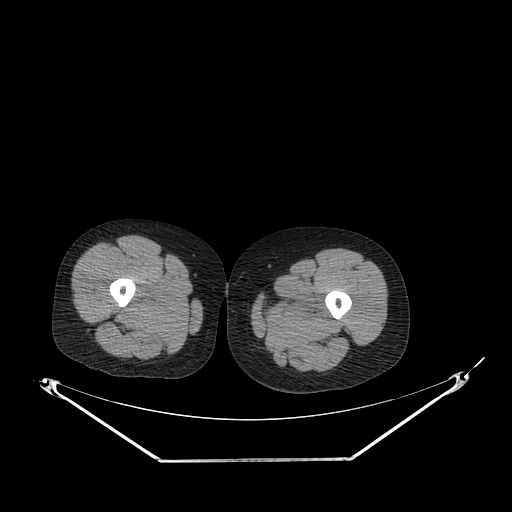
CT of an extremity soft-tissue mass (from a PET/CT study), one axial slice. Slice 222 of 267 in the series (ordered by position). Reconstruction kernel SOFT. 120 kVp. Soft-tissue window (W 400 / L 40 HU). 512 × 512 image matrix. Female patient. Case-level facts recorded for this patient, not image findings: histological type: pleiomorphic leiomyosarcoma; grade: intermediate; site of the primary tumour: left thigh.
Structures marked on this image (expert contour drawn on MRI and transferred to this co-registered scan by the dataset authors):
- gross tumour volume including surrounding oedema: bounding box (x1, y1, x2, y2) in pixels: (263, 292, 325, 316)